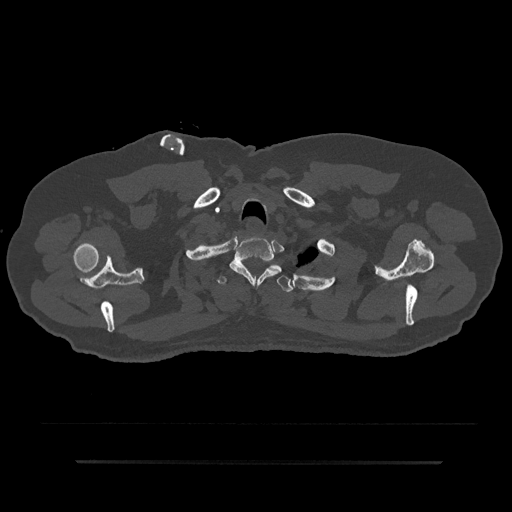
CT including the spine, one axial slice; position 727 of 797 along the scan axis; bone window (W 1800 / L 400 HU); 0.5 mm slice thickness; 512 × 512 image matrix, field of view 464 × 464 mm. Patient: male, 59 years. Case-level facts recorded for this patient, not image findings: primary cancer: bile ducts; vertebrae with lytic lesions (as recorded): T10.
Outlined on this slice (semi-automatic segmentation, software-assisted and operator-edited):
- T1 vertebra: bounding box [x1, y1, x2, y2] px = [229, 236, 278, 285]
- T2 vertebra: [217, 264, 292, 292]